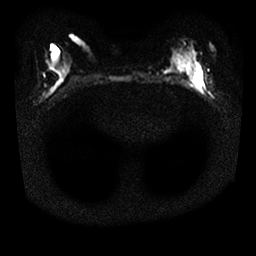
Breast MRI, one axial slice. Position 13 of 25 along the scan axis. Diffusion-weighted series; image 2 of 4 stored at this slice position (different b-values; order by instance number). 1.5 T. 4 mm slice thickness. 256 × 256 image matrix, field of view 310 × 310 mm. Female patient.
Outlined on this slice (manually delineated by an expert):
- tumour on diffusion-weighted imaging: bounding box [x1, y1, x2, y2] px = [192, 74, 202, 85]